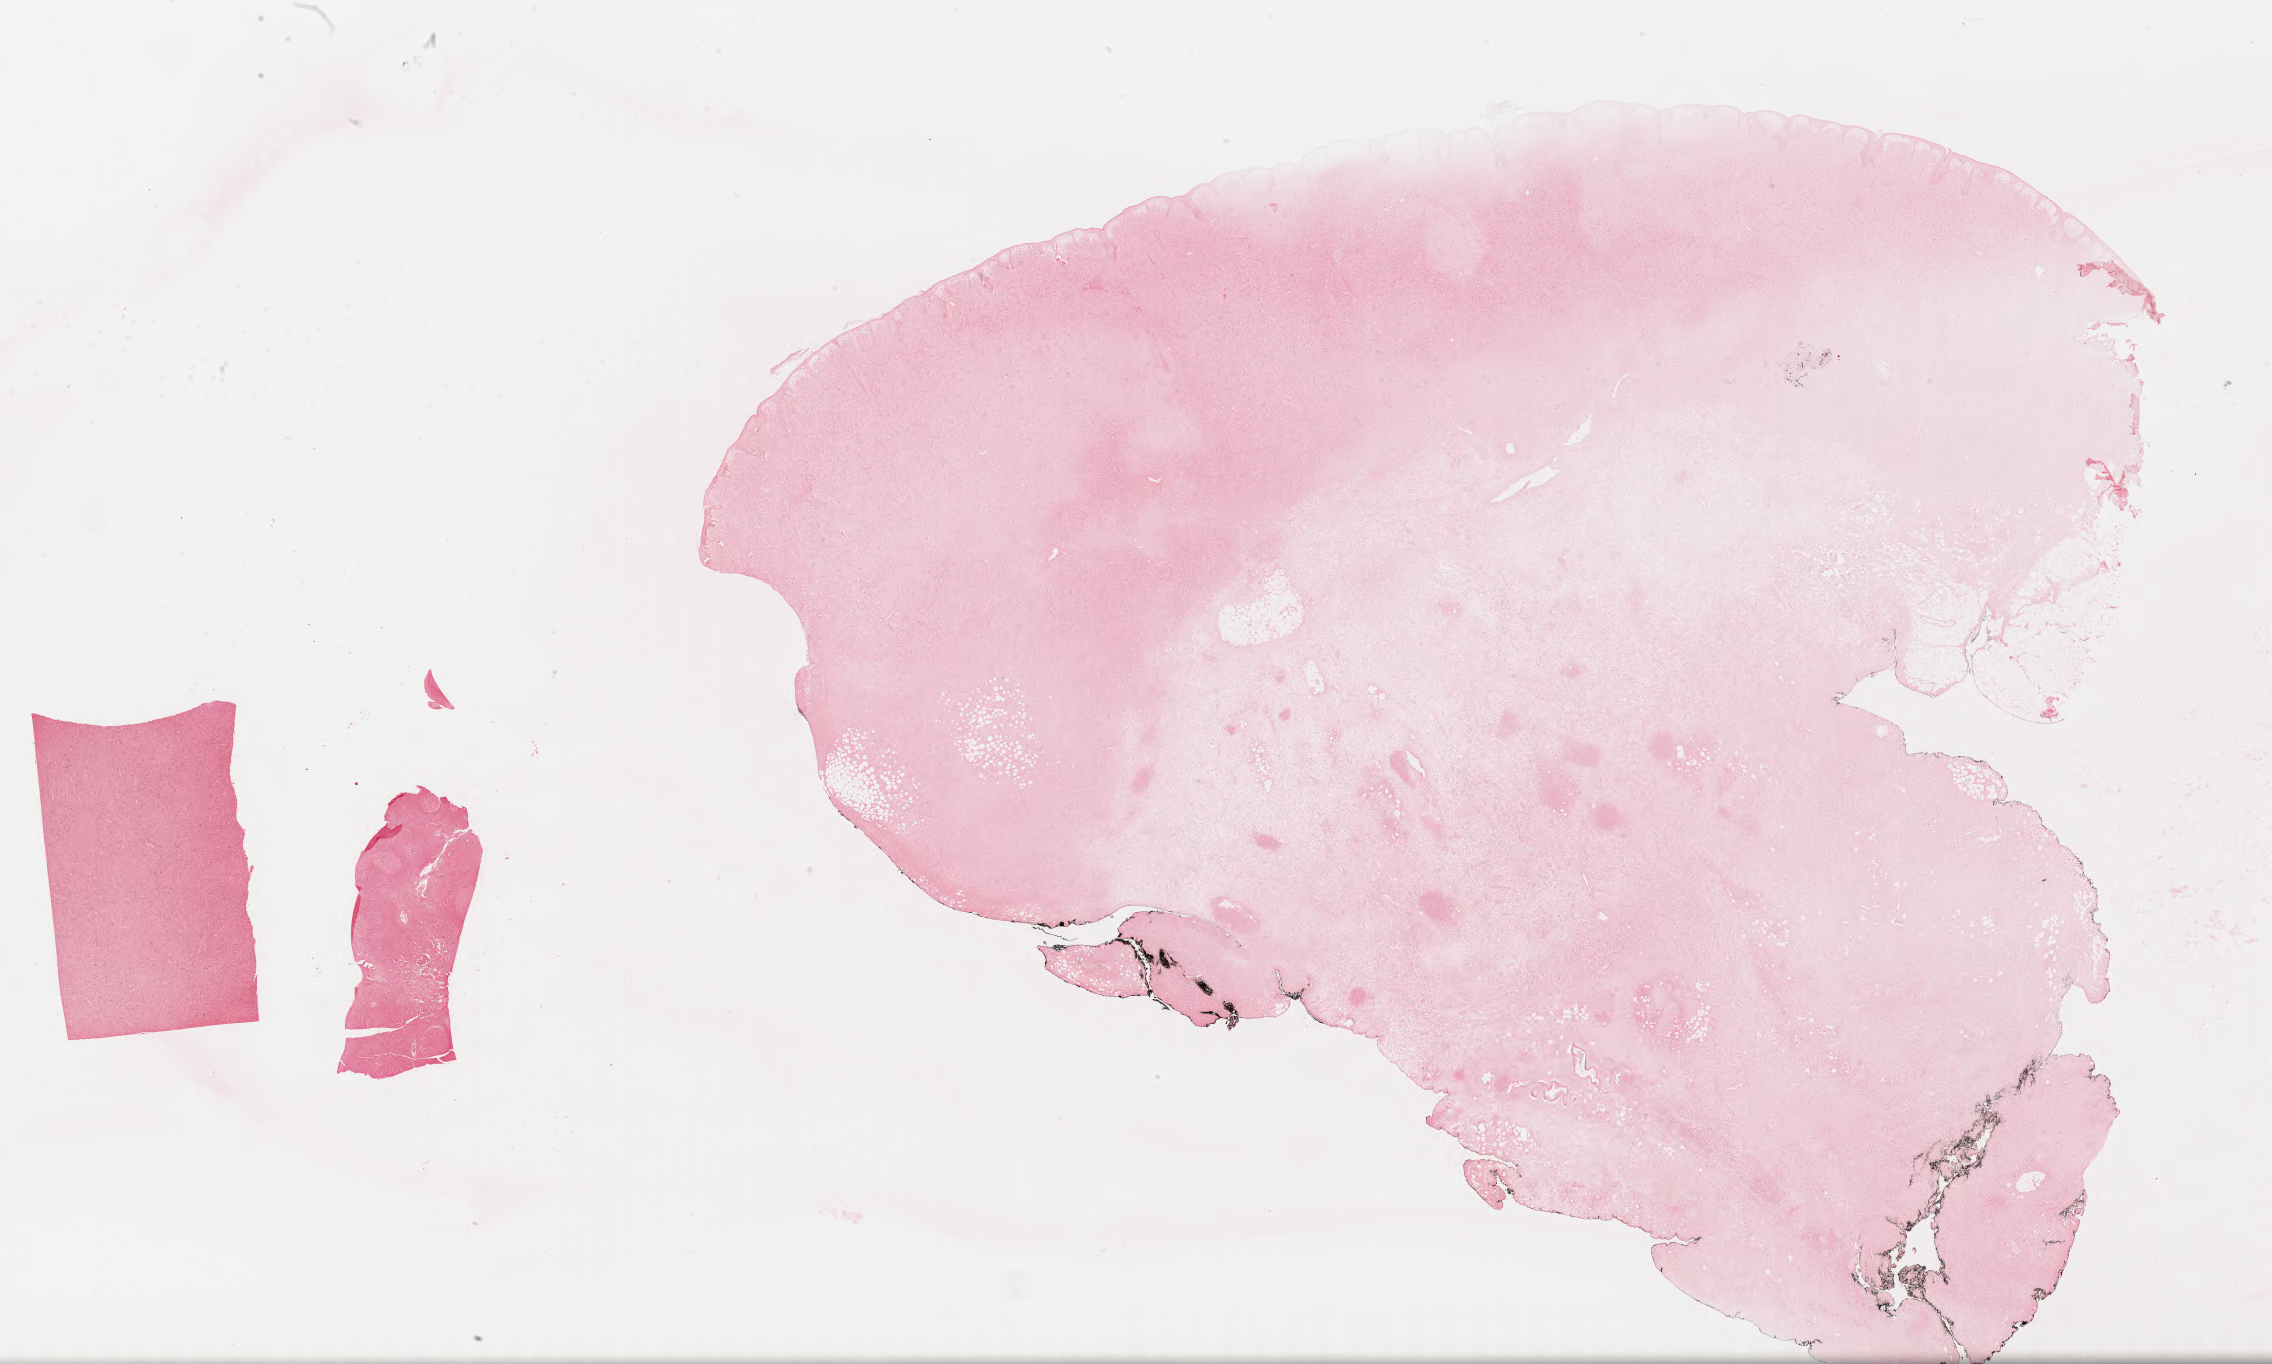
In-situ hybridisation whole-slide image, Epstein–Barr virus-encoded RNA (EBER) probe, a low-resolution overview of the entire scanned area, about 36.7 x 22.0 mm; specimen: tumor tissue; site: lymph node. Male patient, aged 52.
* diagnosis: Diffuse large B-cell lymphoma, NOS